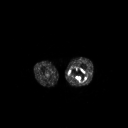
FDG PET of an extremity soft-tissue mass (from a PET/CT study), one axial slice. Slice 215 of 267 in the series (ordered by position). 3.27 mm slice thickness. 128 × 128 image matrix, field of view 700 × 700 mm. Patient: male, 44 years. Case-level facts recorded for this patient, not image findings: histological type: undifferentiated pleomorphic liposarcoma; grade: high; site of the primary tumour: left thigh.
Outlined on this slice (expert contour drawn on MRI and transferred to this co-registered scan by the dataset authors):
- gross tumour volume including surrounding oedema: bounding box [x1, y1, x2, y2] px = [69, 66, 87, 83]
- gross tumour volume (mass): [69, 68, 87, 82]